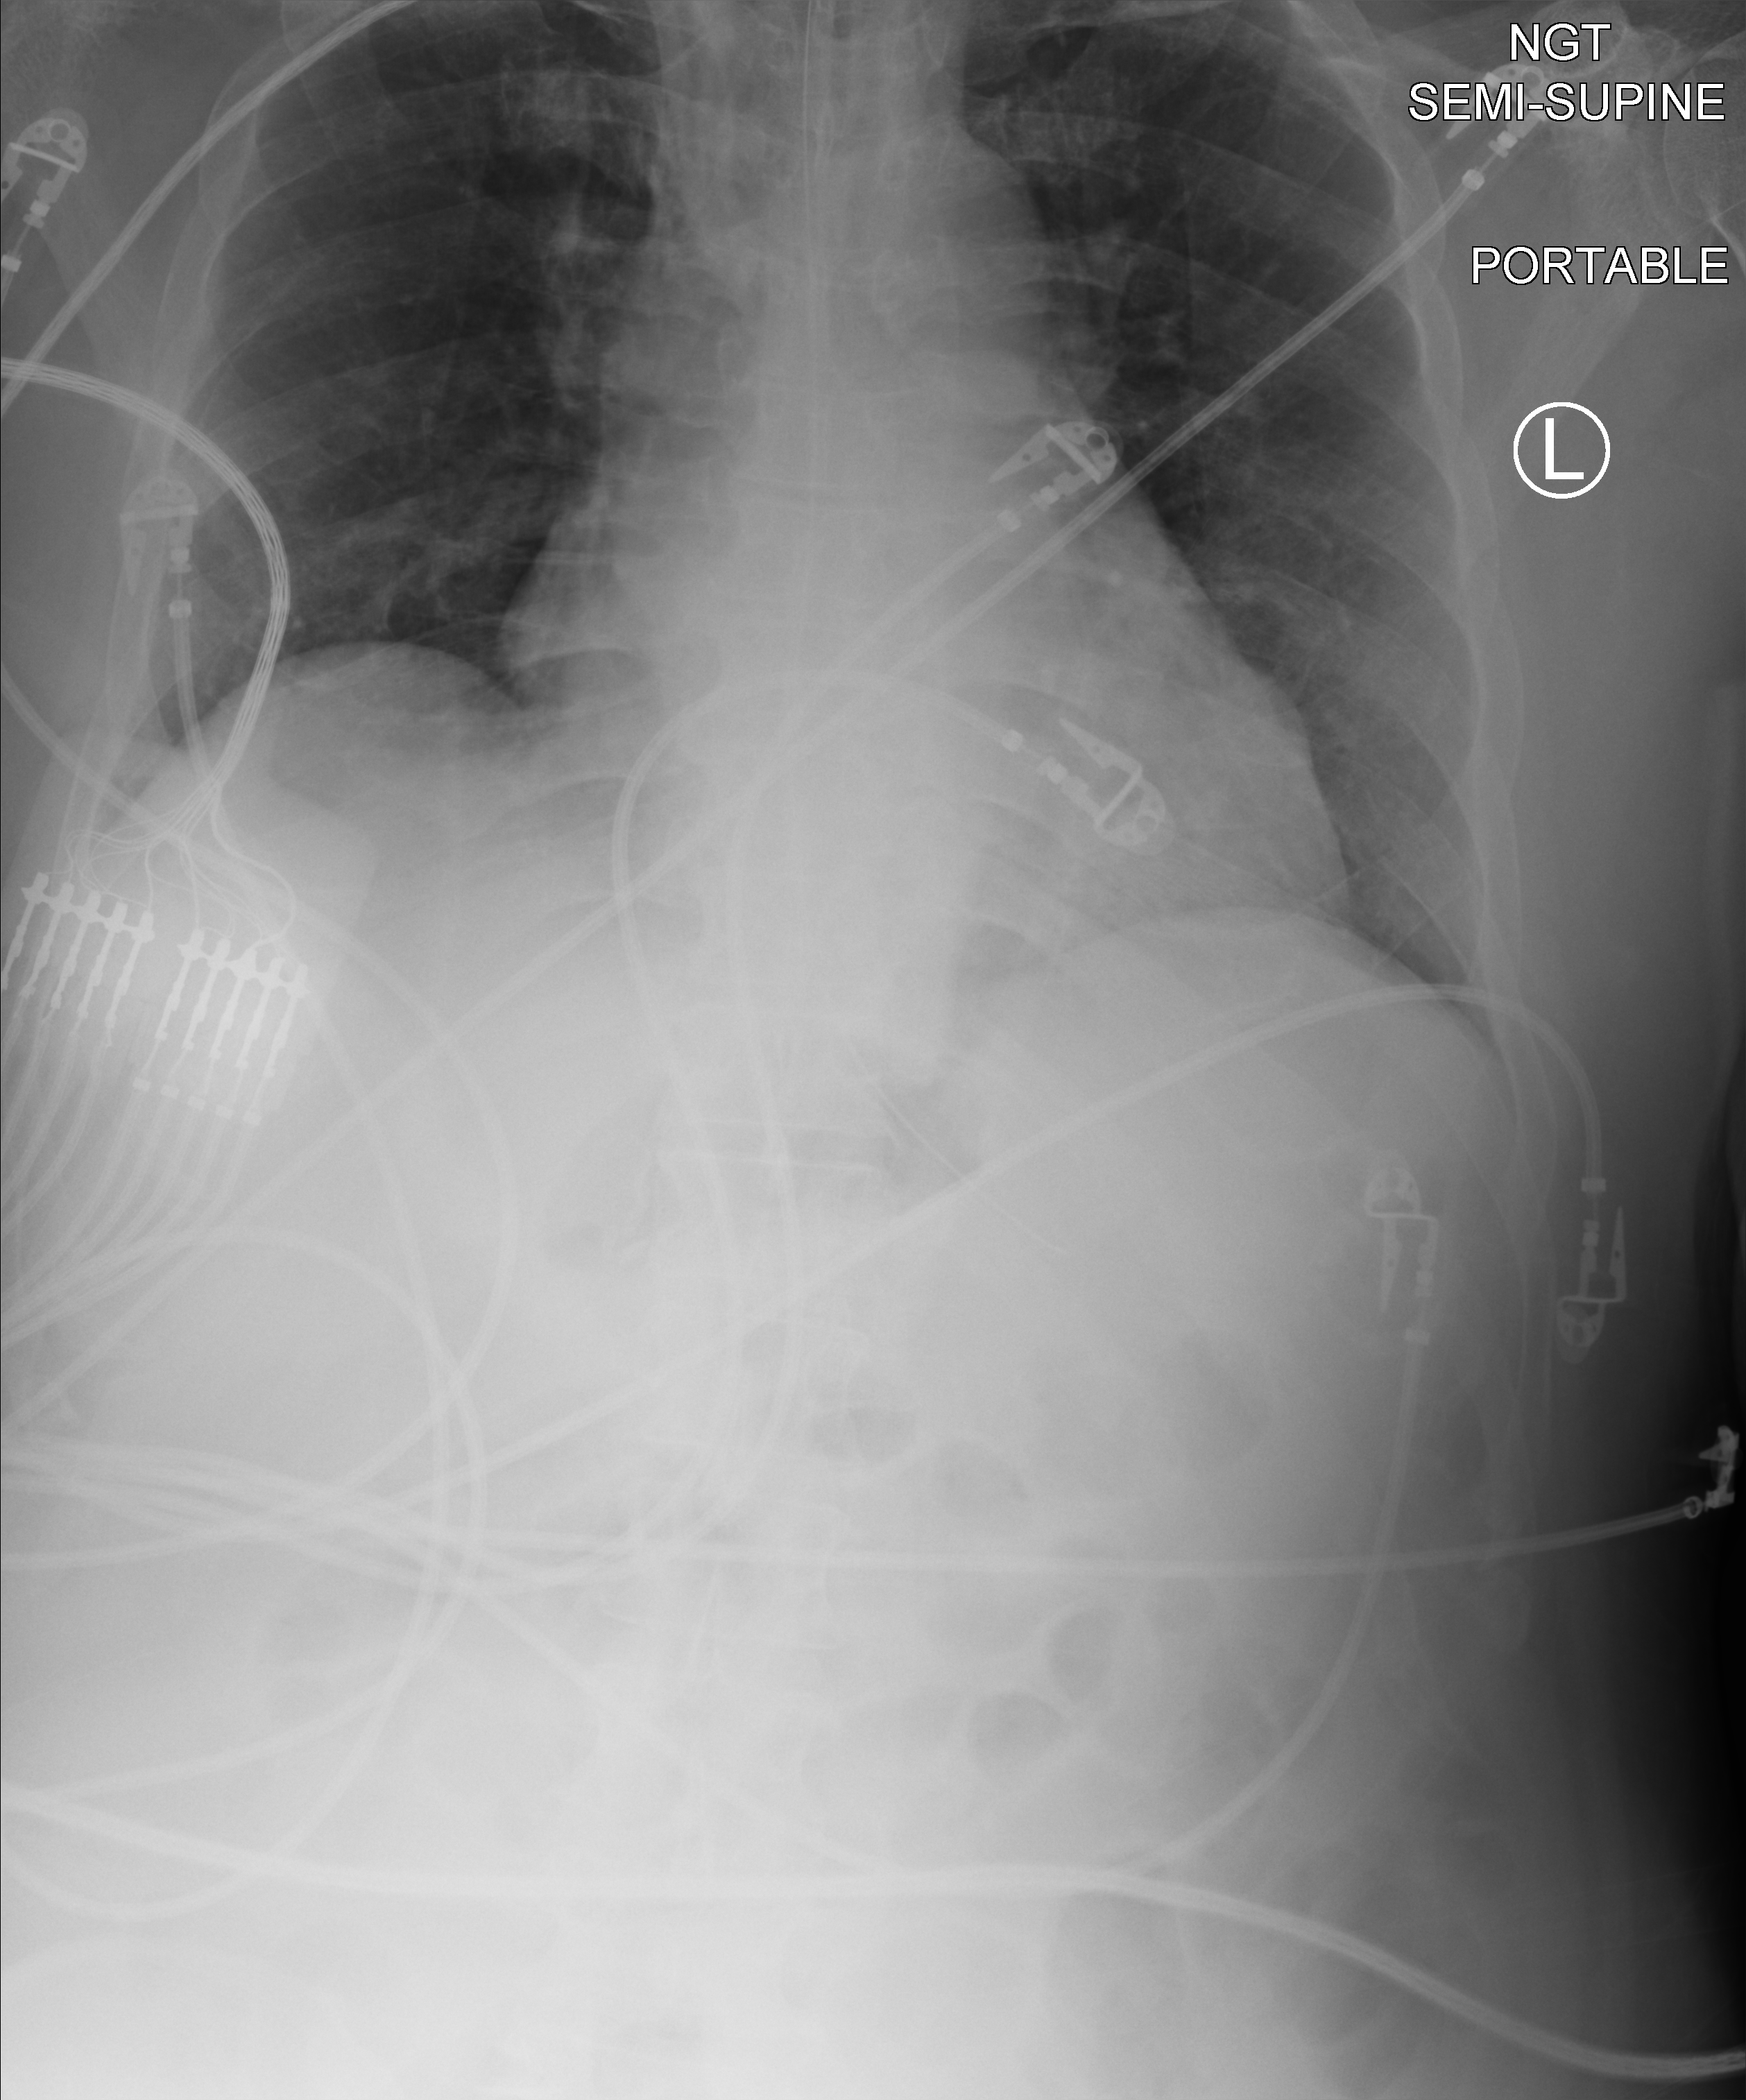
Portable chest radiograph; anteroposterior (AP) projection. Adult patient hospitalised with COVID-19, age 18–59 years.
Hospital-stay facts (about this admission, not read from this image; timing relative to this image not recorded):
- other chronic lung disease (admission record): no
- length of hospital stay: 37 days